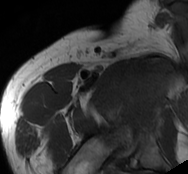
MRI of an extremity soft-tissue mass, one axial slice; position 73 of 93 along the scan axis; MR volume resampled by the dataset authors to the PET/CT grid (not the native acquisition matrix); 3.27 mm slice thickness; 188 × 174 image matrix. Male patient. From the clinical record (not read from this slice): histological type: undifferentiated - pleiomorphic; grade: high; site of the primary tumour: right thigh.
Outlined on this slice (expert contour drawn on MRI and transferred to this co-registered scan by the dataset authors):
- gross tumour volume including surrounding oedema: bounding box (x1, y1, x2, y2) in pixels: (120, 60, 174, 113)
- gross tumour volume (mass): (123, 69, 164, 107)